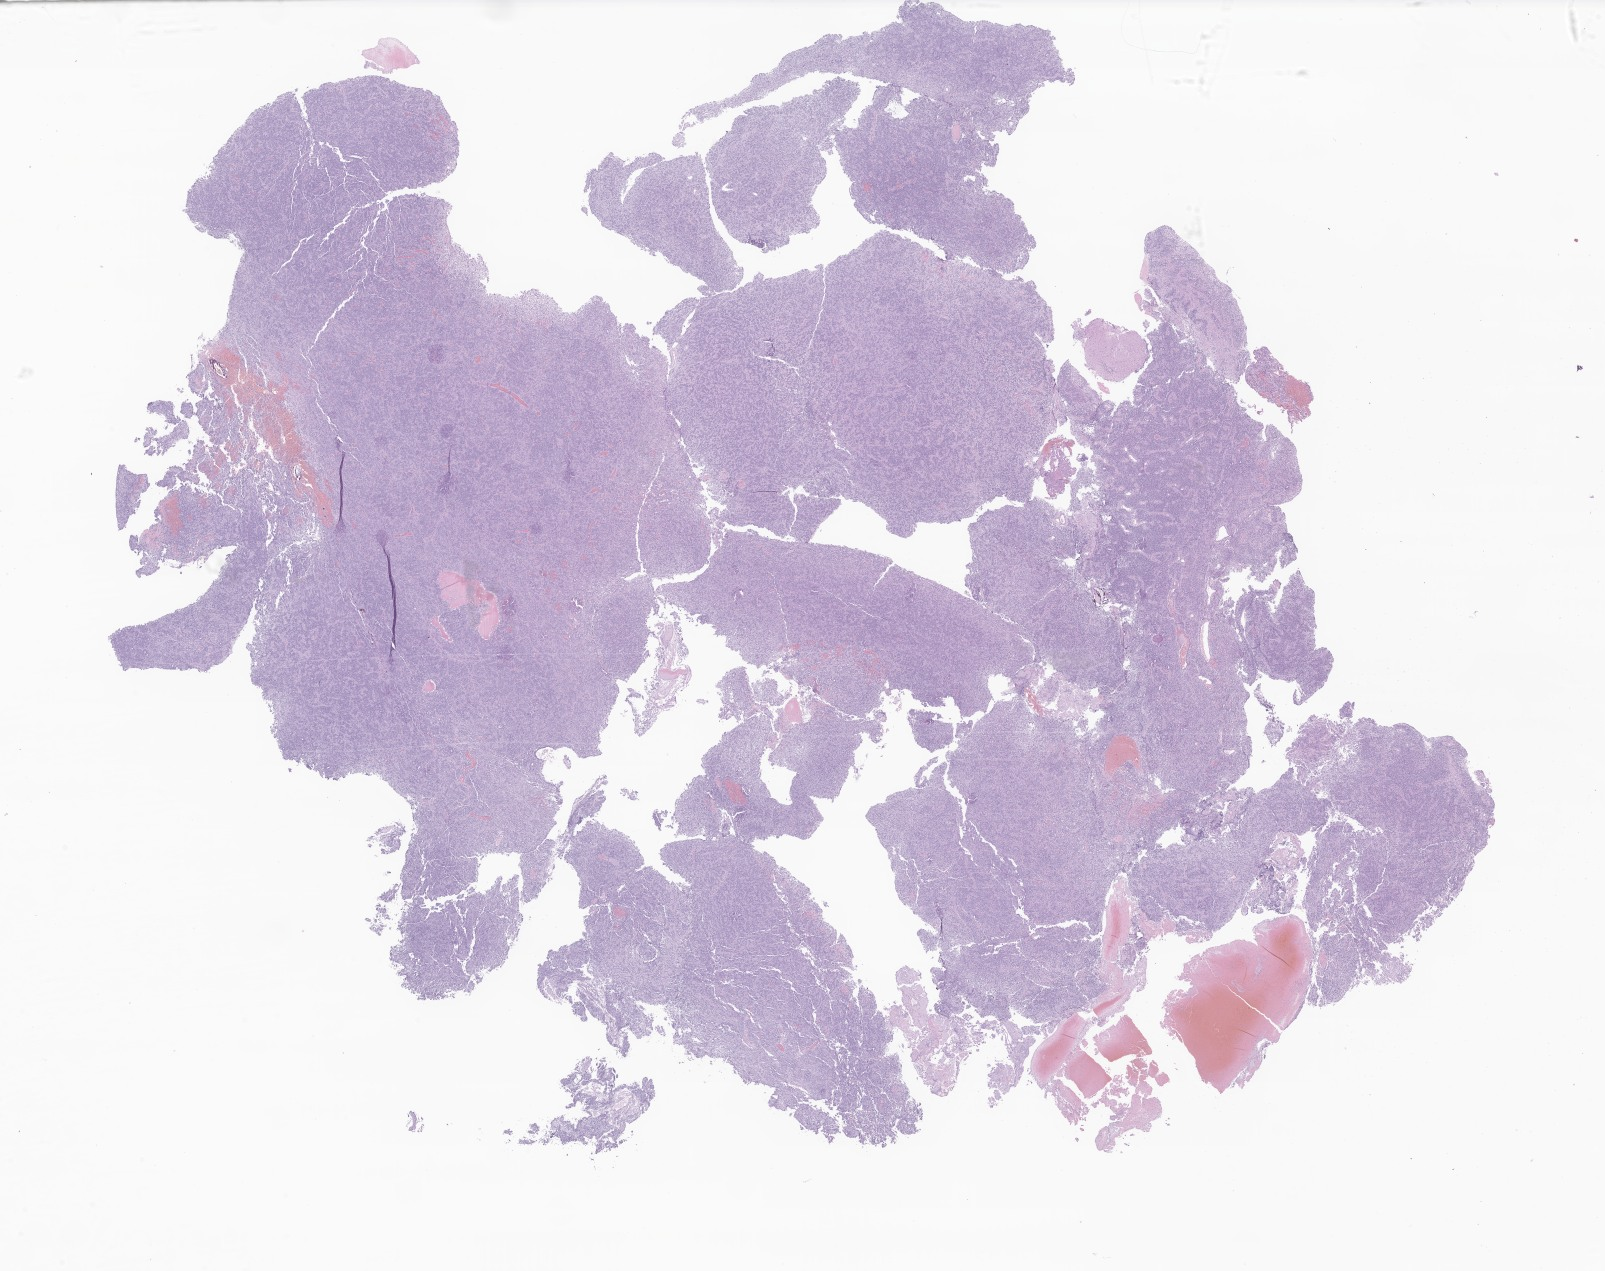
Digitized haematoxylin and eosin-stained section of tumor tissue from the brain — a low-resolution overview of the entire scanned area, about 27.1 x 21.4 mm, formalin-fixed paraffin-embedded section. Patient: female, age 55 months (4 years 7 months).
Diagnosis (ICD-O-3 morphology term): Ependymoma, NOS.